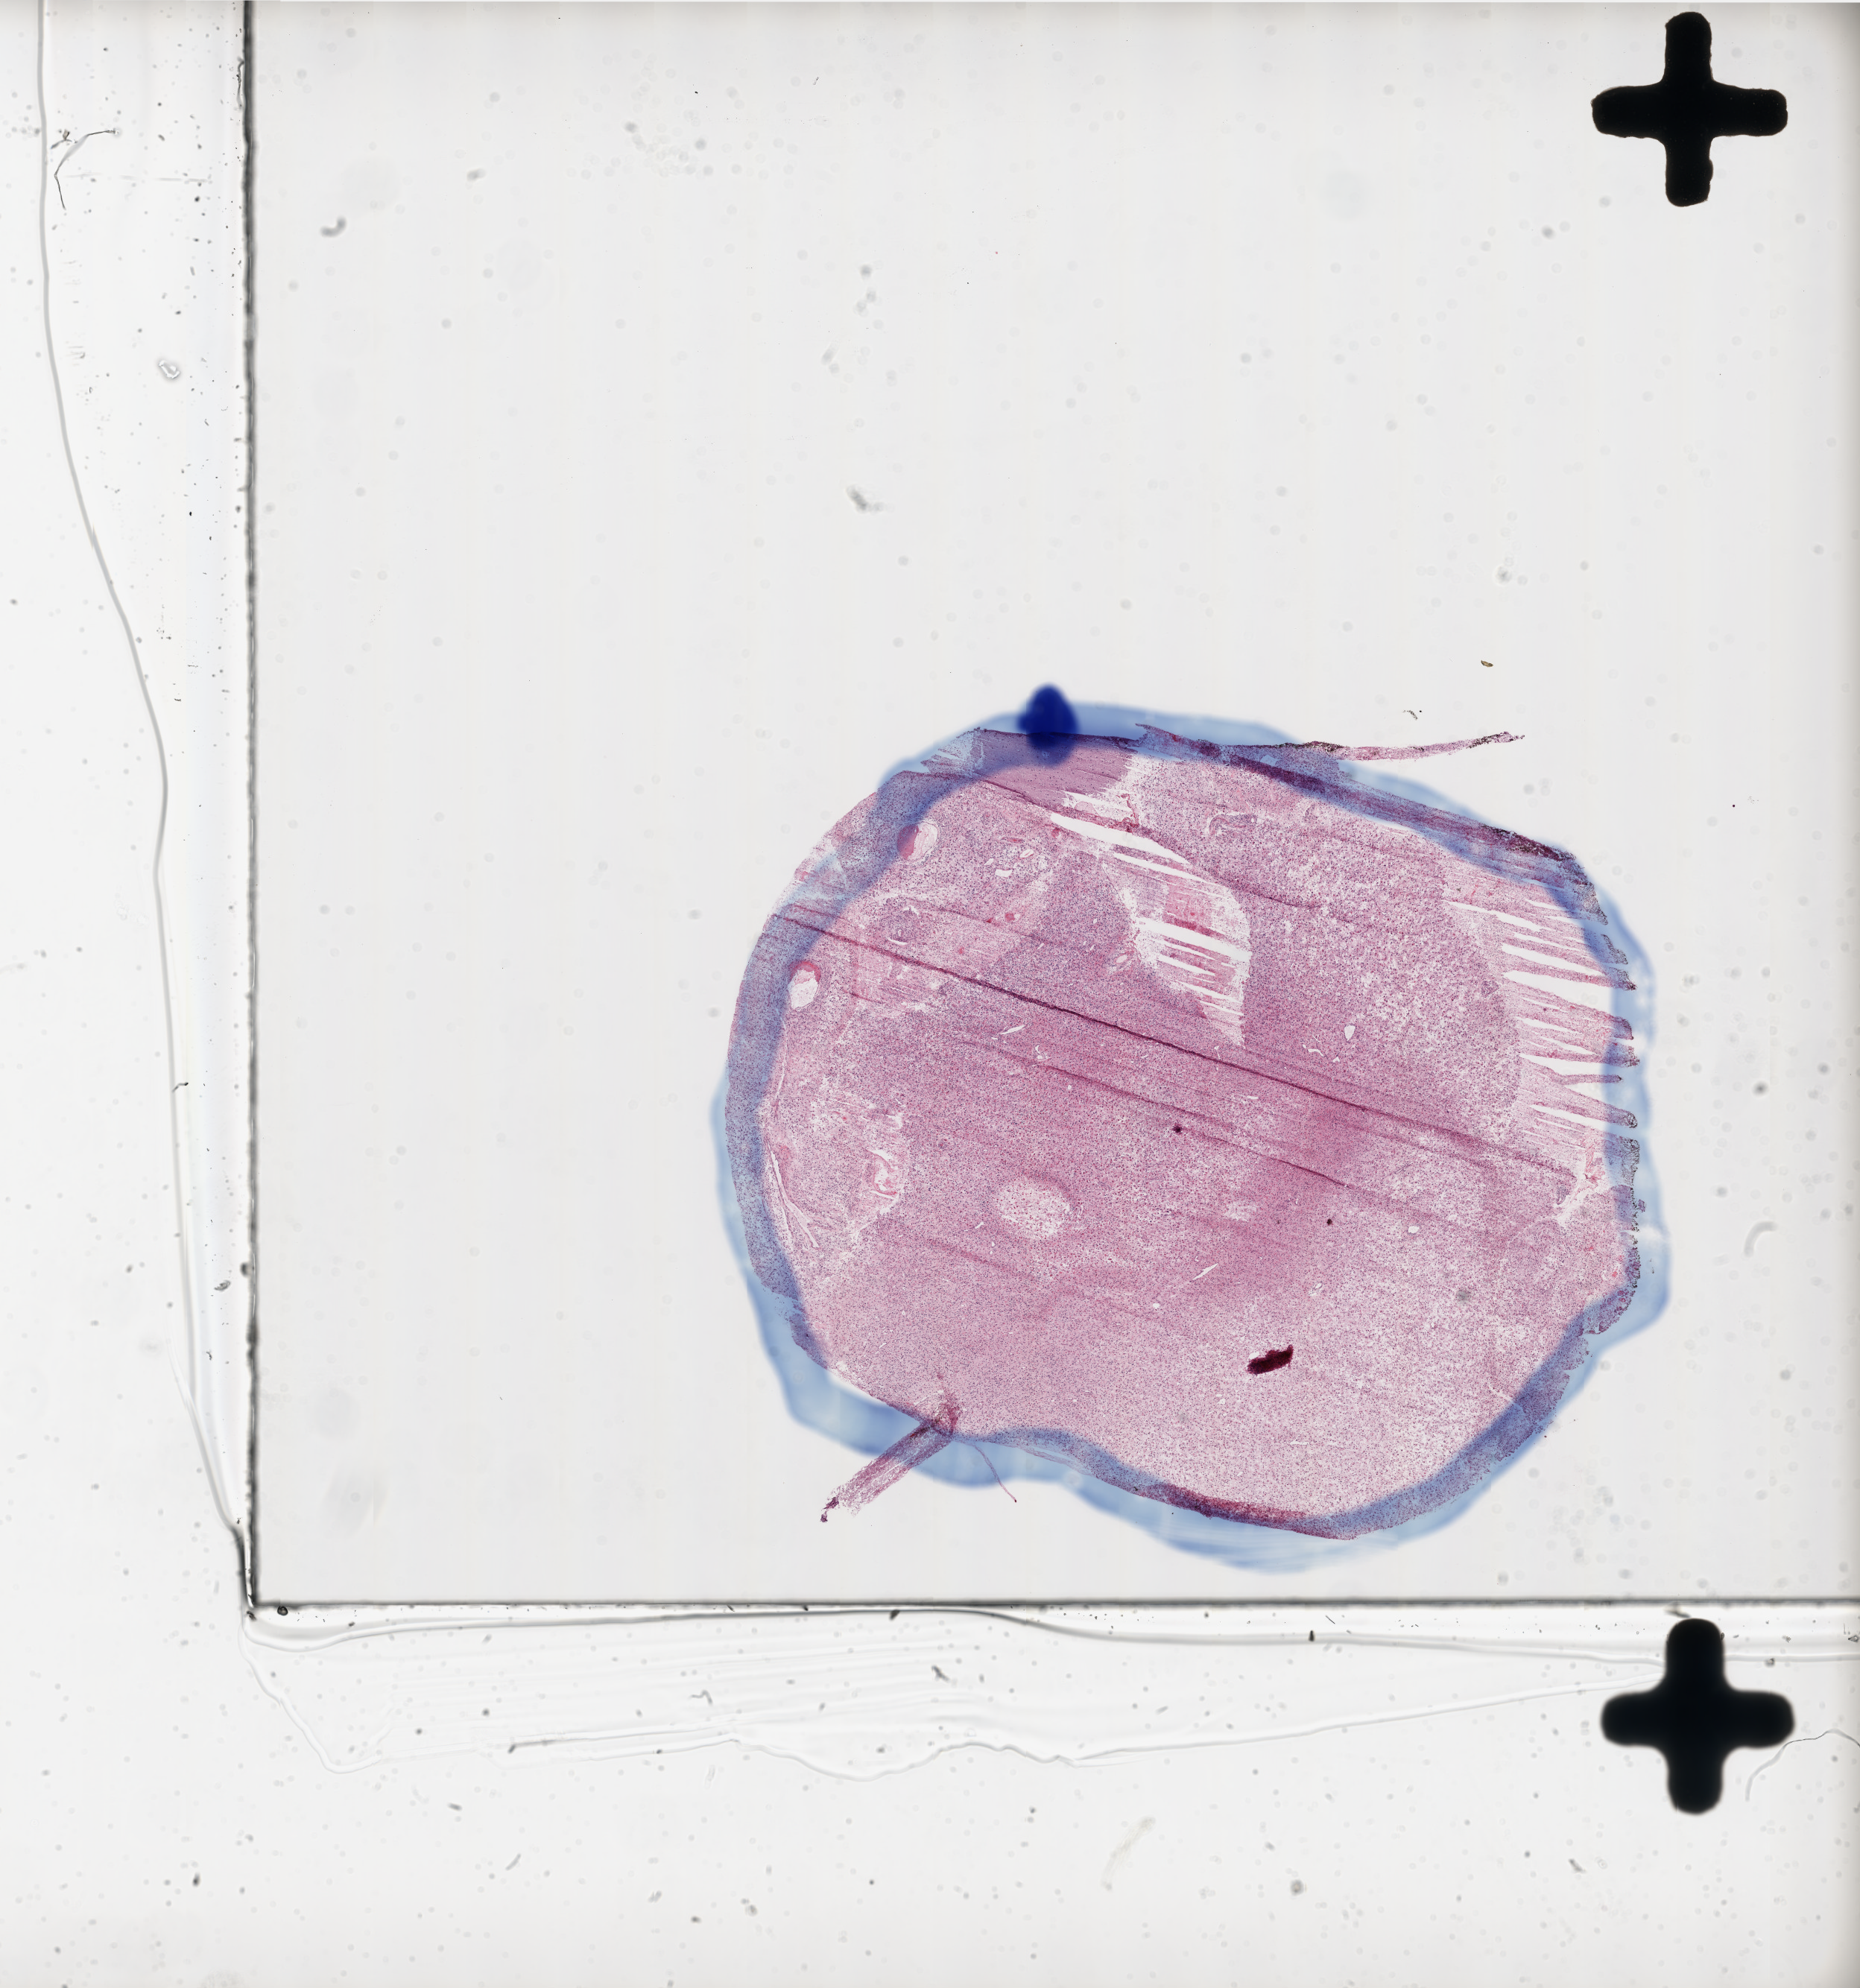
Digitized H&E tissue section (whole slide) — a low-resolution overview of the entire scanned area, about 20.0 x 21.4 mm (from a 20x scan); frozen section from the top of the tissue portion; brain, primary tumour sample. Patient: male, age at initial diagnosis 43 years. Pathologist review of this section (percent, as recorded): tumour cells 85%, tumour nuclei 100%, normal cells 5%, stromal cells 0%, necrosis 10%. Infiltration values recorded for this section: lymphocyte infiltration 0%, monocyte infiltration 0%, neutrophil infiltration 0%.
Diagnosis: Glioblastoma.